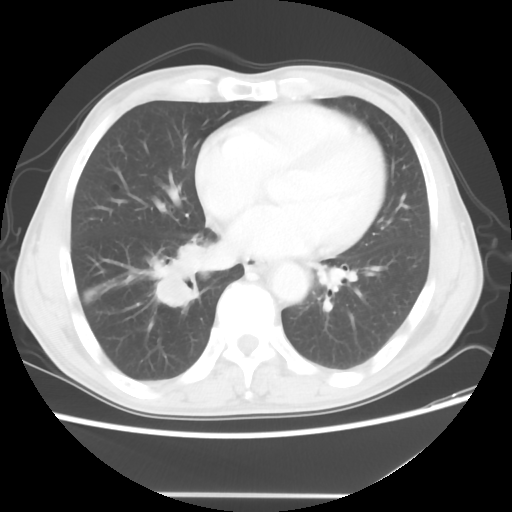
Chest CT, one axial slice. Slice 22 of 56 in the series (ordered by position). Lung window (W 1500 / L -600 HU). 5 mm slice thickness. 512 × 512 image matrix, field of view 344 × 344 mm. Male patient, age 65 years. From the clinical record (not read from this slice): clinical TNM (as recorded): T1c N3 M0; histopathological grade: G3.
Structures marked on this image (bounding box drawn by a radiologist):
- lung tumour (recorded histology: small cell carcinoma): bounding box [x1, y1, x2, y2] px = [151, 242, 203, 307]